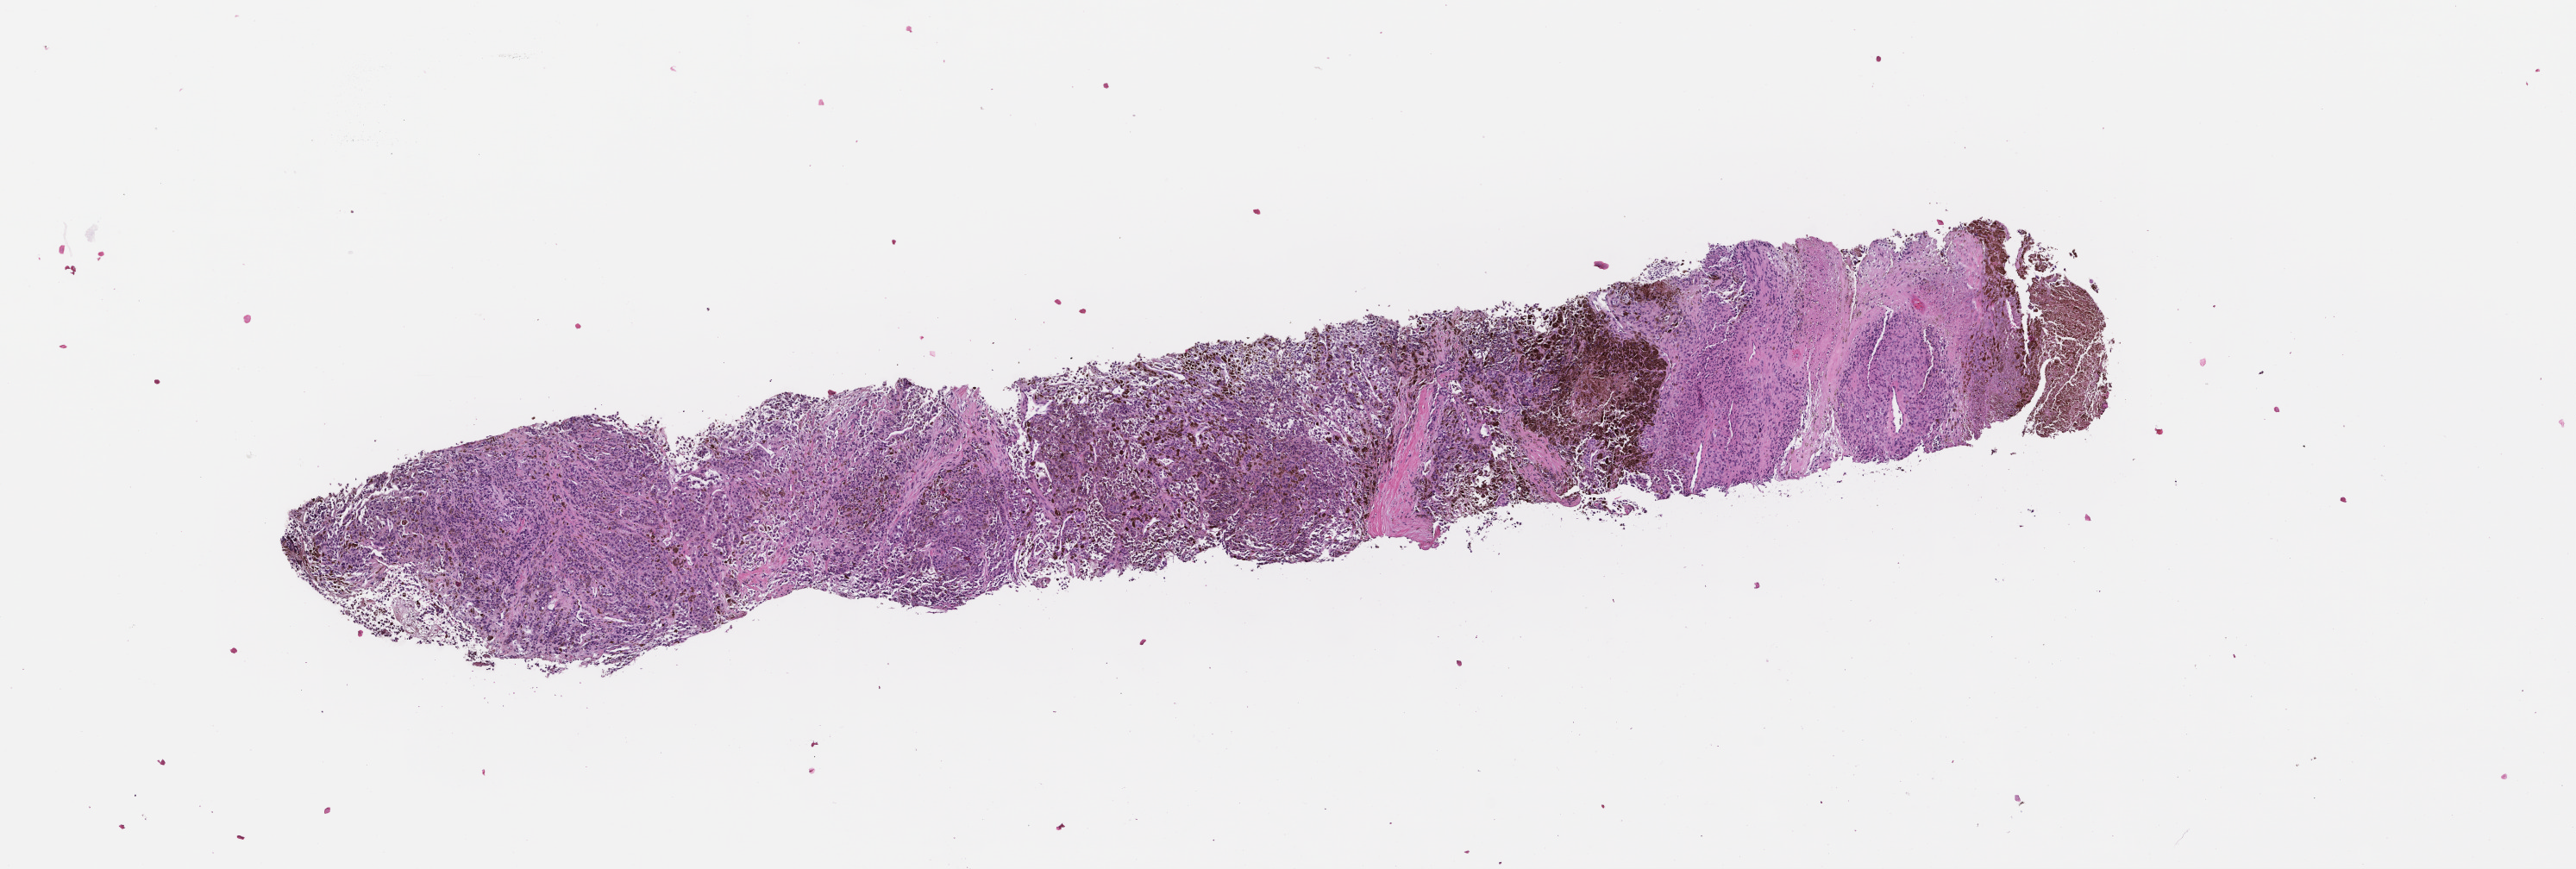
Digitized hematoxylin and eosin (H&E)-stained section, whole scanned area (about 12.1 x 4.1 mm) shown as a low-resolution overview; formalin-fixed, paraffin-embedded (FFPE) tissue; specimen time point: collected at baseline (before treatment). Patient: female.
This section: metastatic tumor tissue. Patient diagnosis (primary): Melanoma.